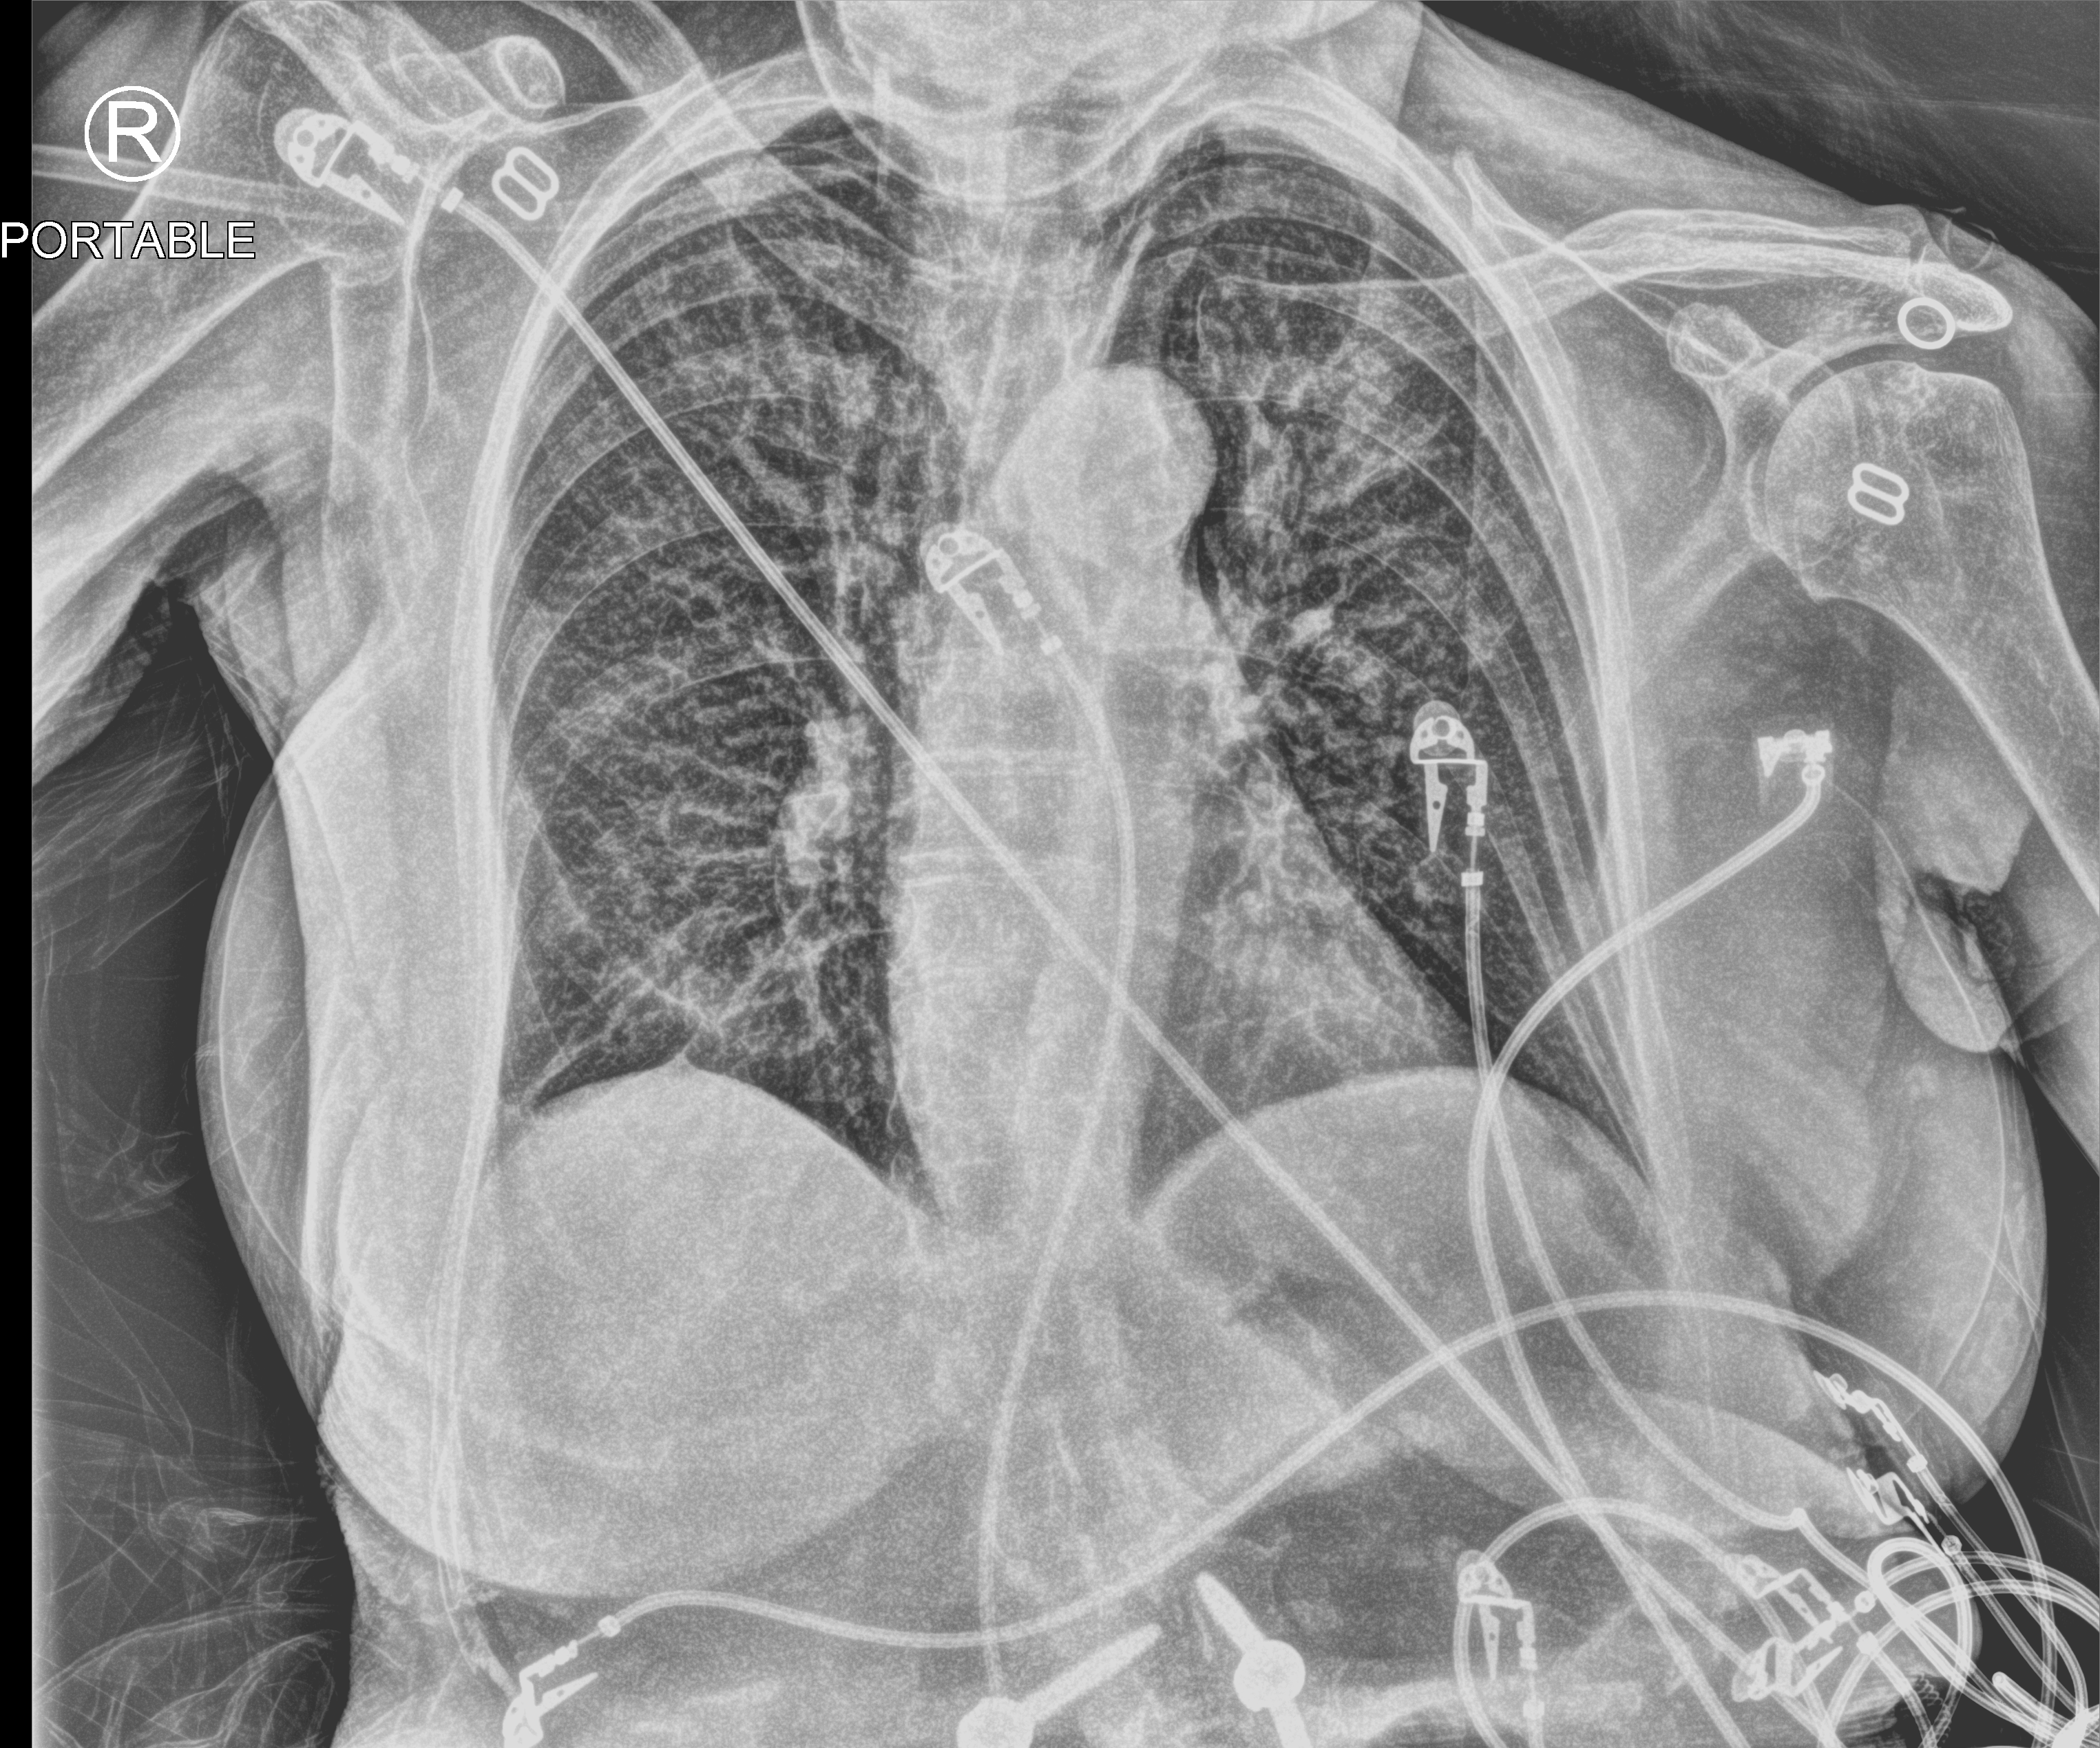
Portable chest radiograph. Patient hospitalised with COVID-19; female, aged 60–74 years.
Hospital-stay facts (about this admission, not read from this image; timing relative to this image not recorded): admitted to intensive care during this hospital stay: no; mechanically ventilated during this hospital stay: no.